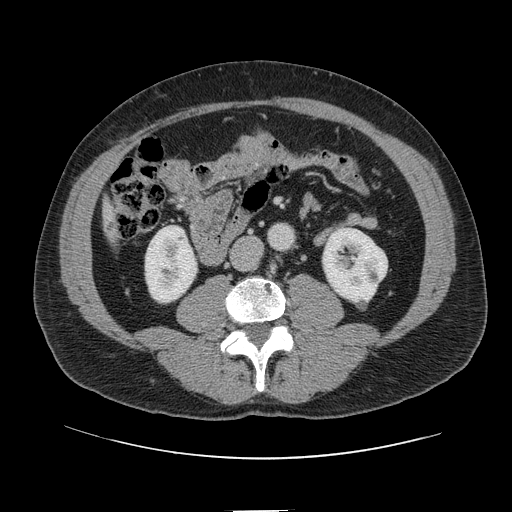
Contrast-enhanced abdominal CT, one axial slice; position 10 of 161 along the scan axis; intravenous contrast given; soft-tissue window (W 400 / L 40 HU); 2.5 mm slice thickness; 512 × 512 image matrix, field of view 412 × 412 mm. Male patient, age 66 years. Case-level facts recorded for this patient, not image findings: diagnosis: colorectal cancer liver metastases, imaged before liver resection; multiple liver metastases: no; largest metastasis: 3.5 cm.
Annotated regions visible in this slice (manually delineated by an expert):
- liver: box from (x=106, y=210) to (x=116, y=242) px
- planned liver remnant (the part of the liver to remain after resection): (x=106, y=209)–(x=115, y=232)